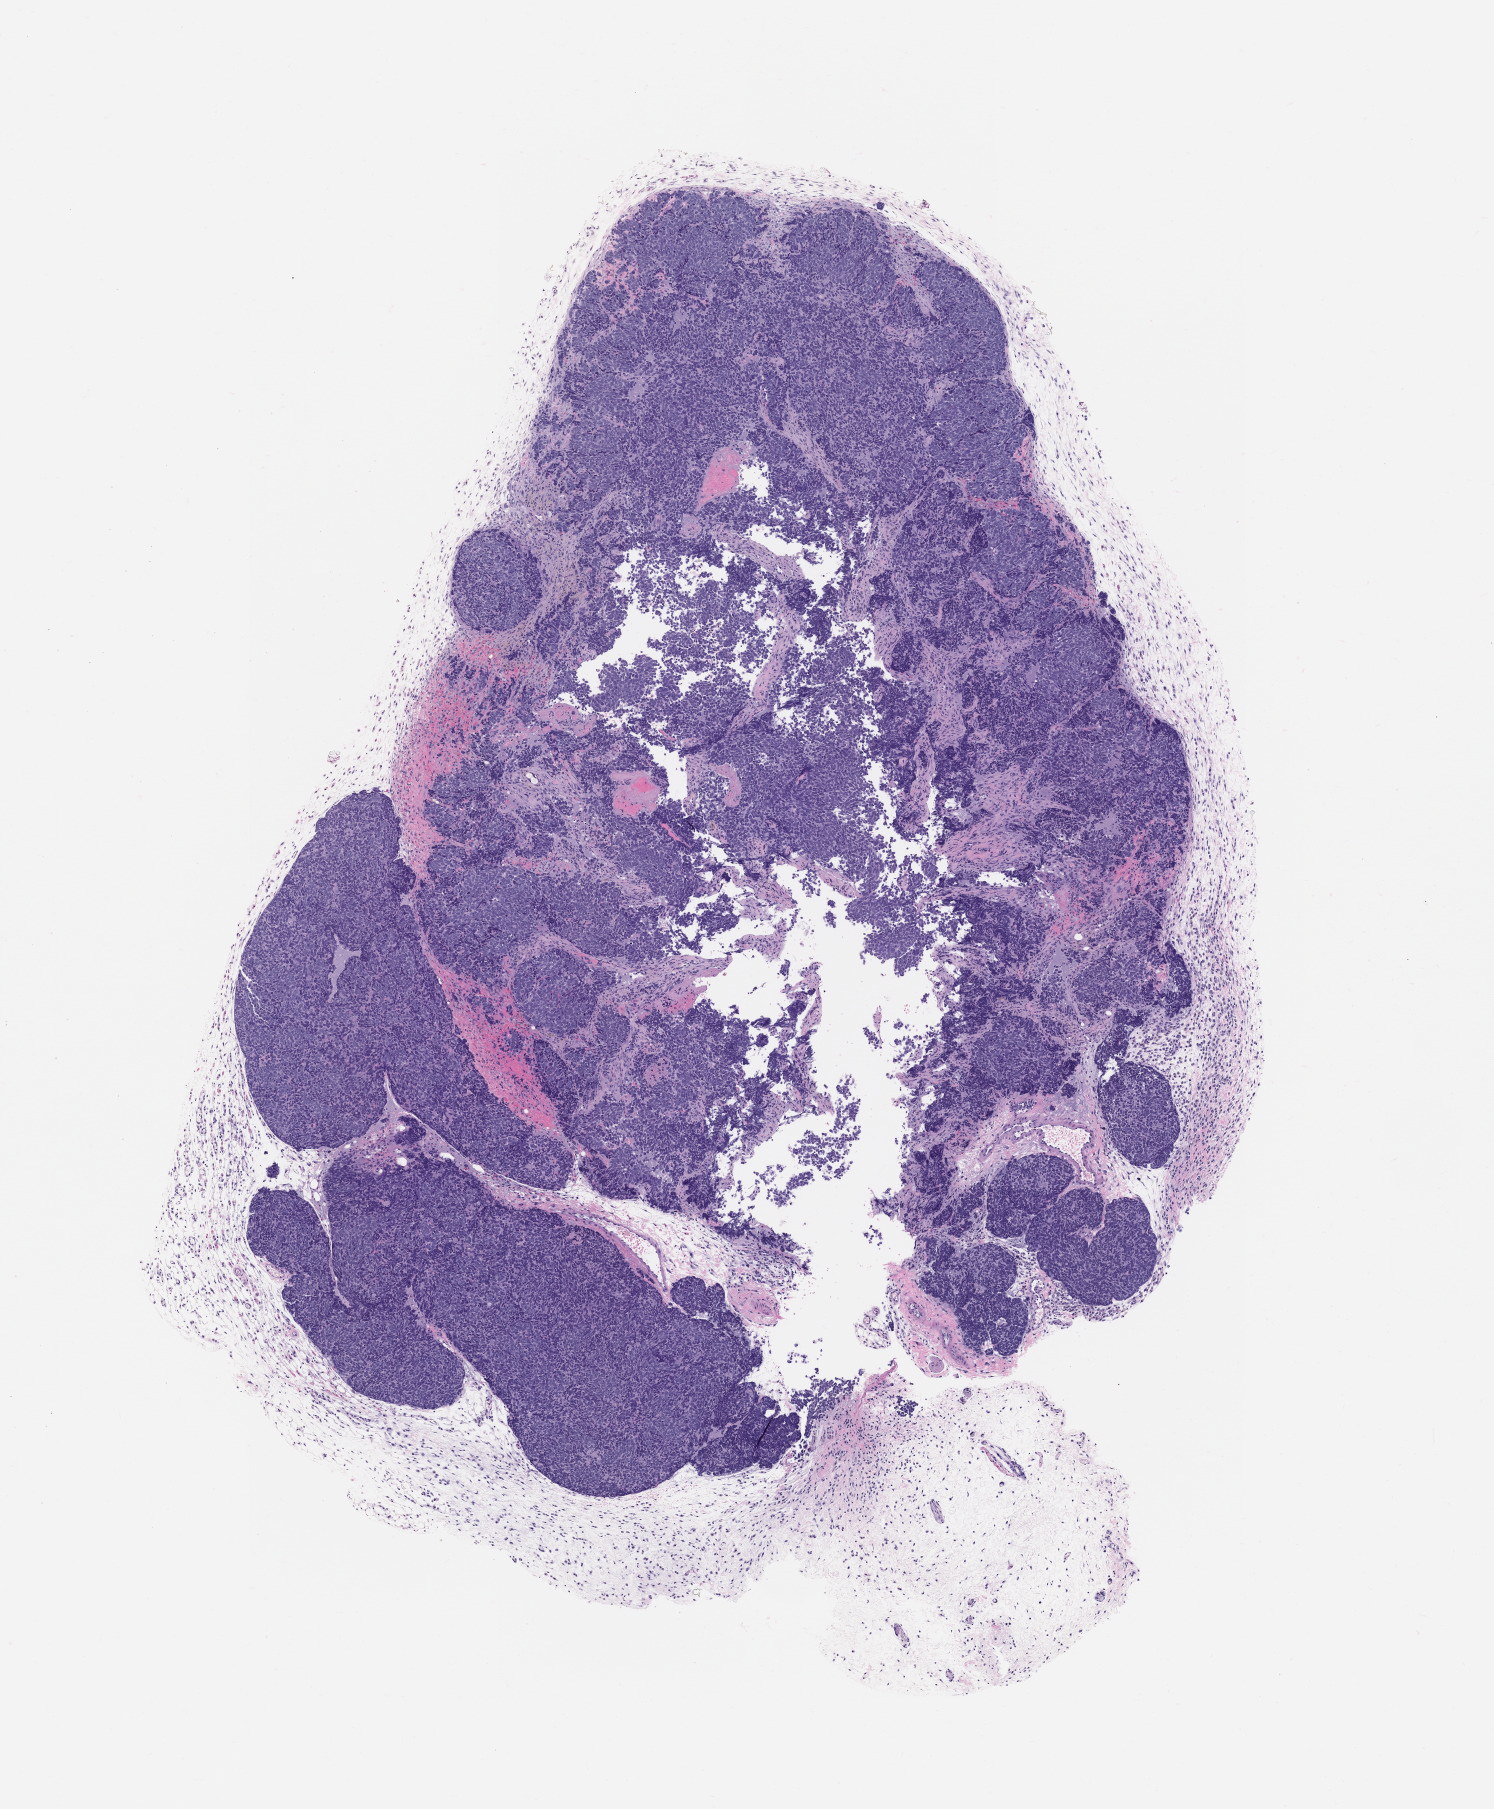
Whole-slide image, haematoxylin and eosin: patient-derived xenograft (human tumor grown in a mouse), passage 1 — low-resolution overview of the scanned area, about 6.0 x 7.3 mm; formalin-fixed, paraffin-embedded (FFPE) tissue; tumor site category: bladder.
- originating patient diagnosis: Bladder Small Cell Neuroendocrine Carcinoma